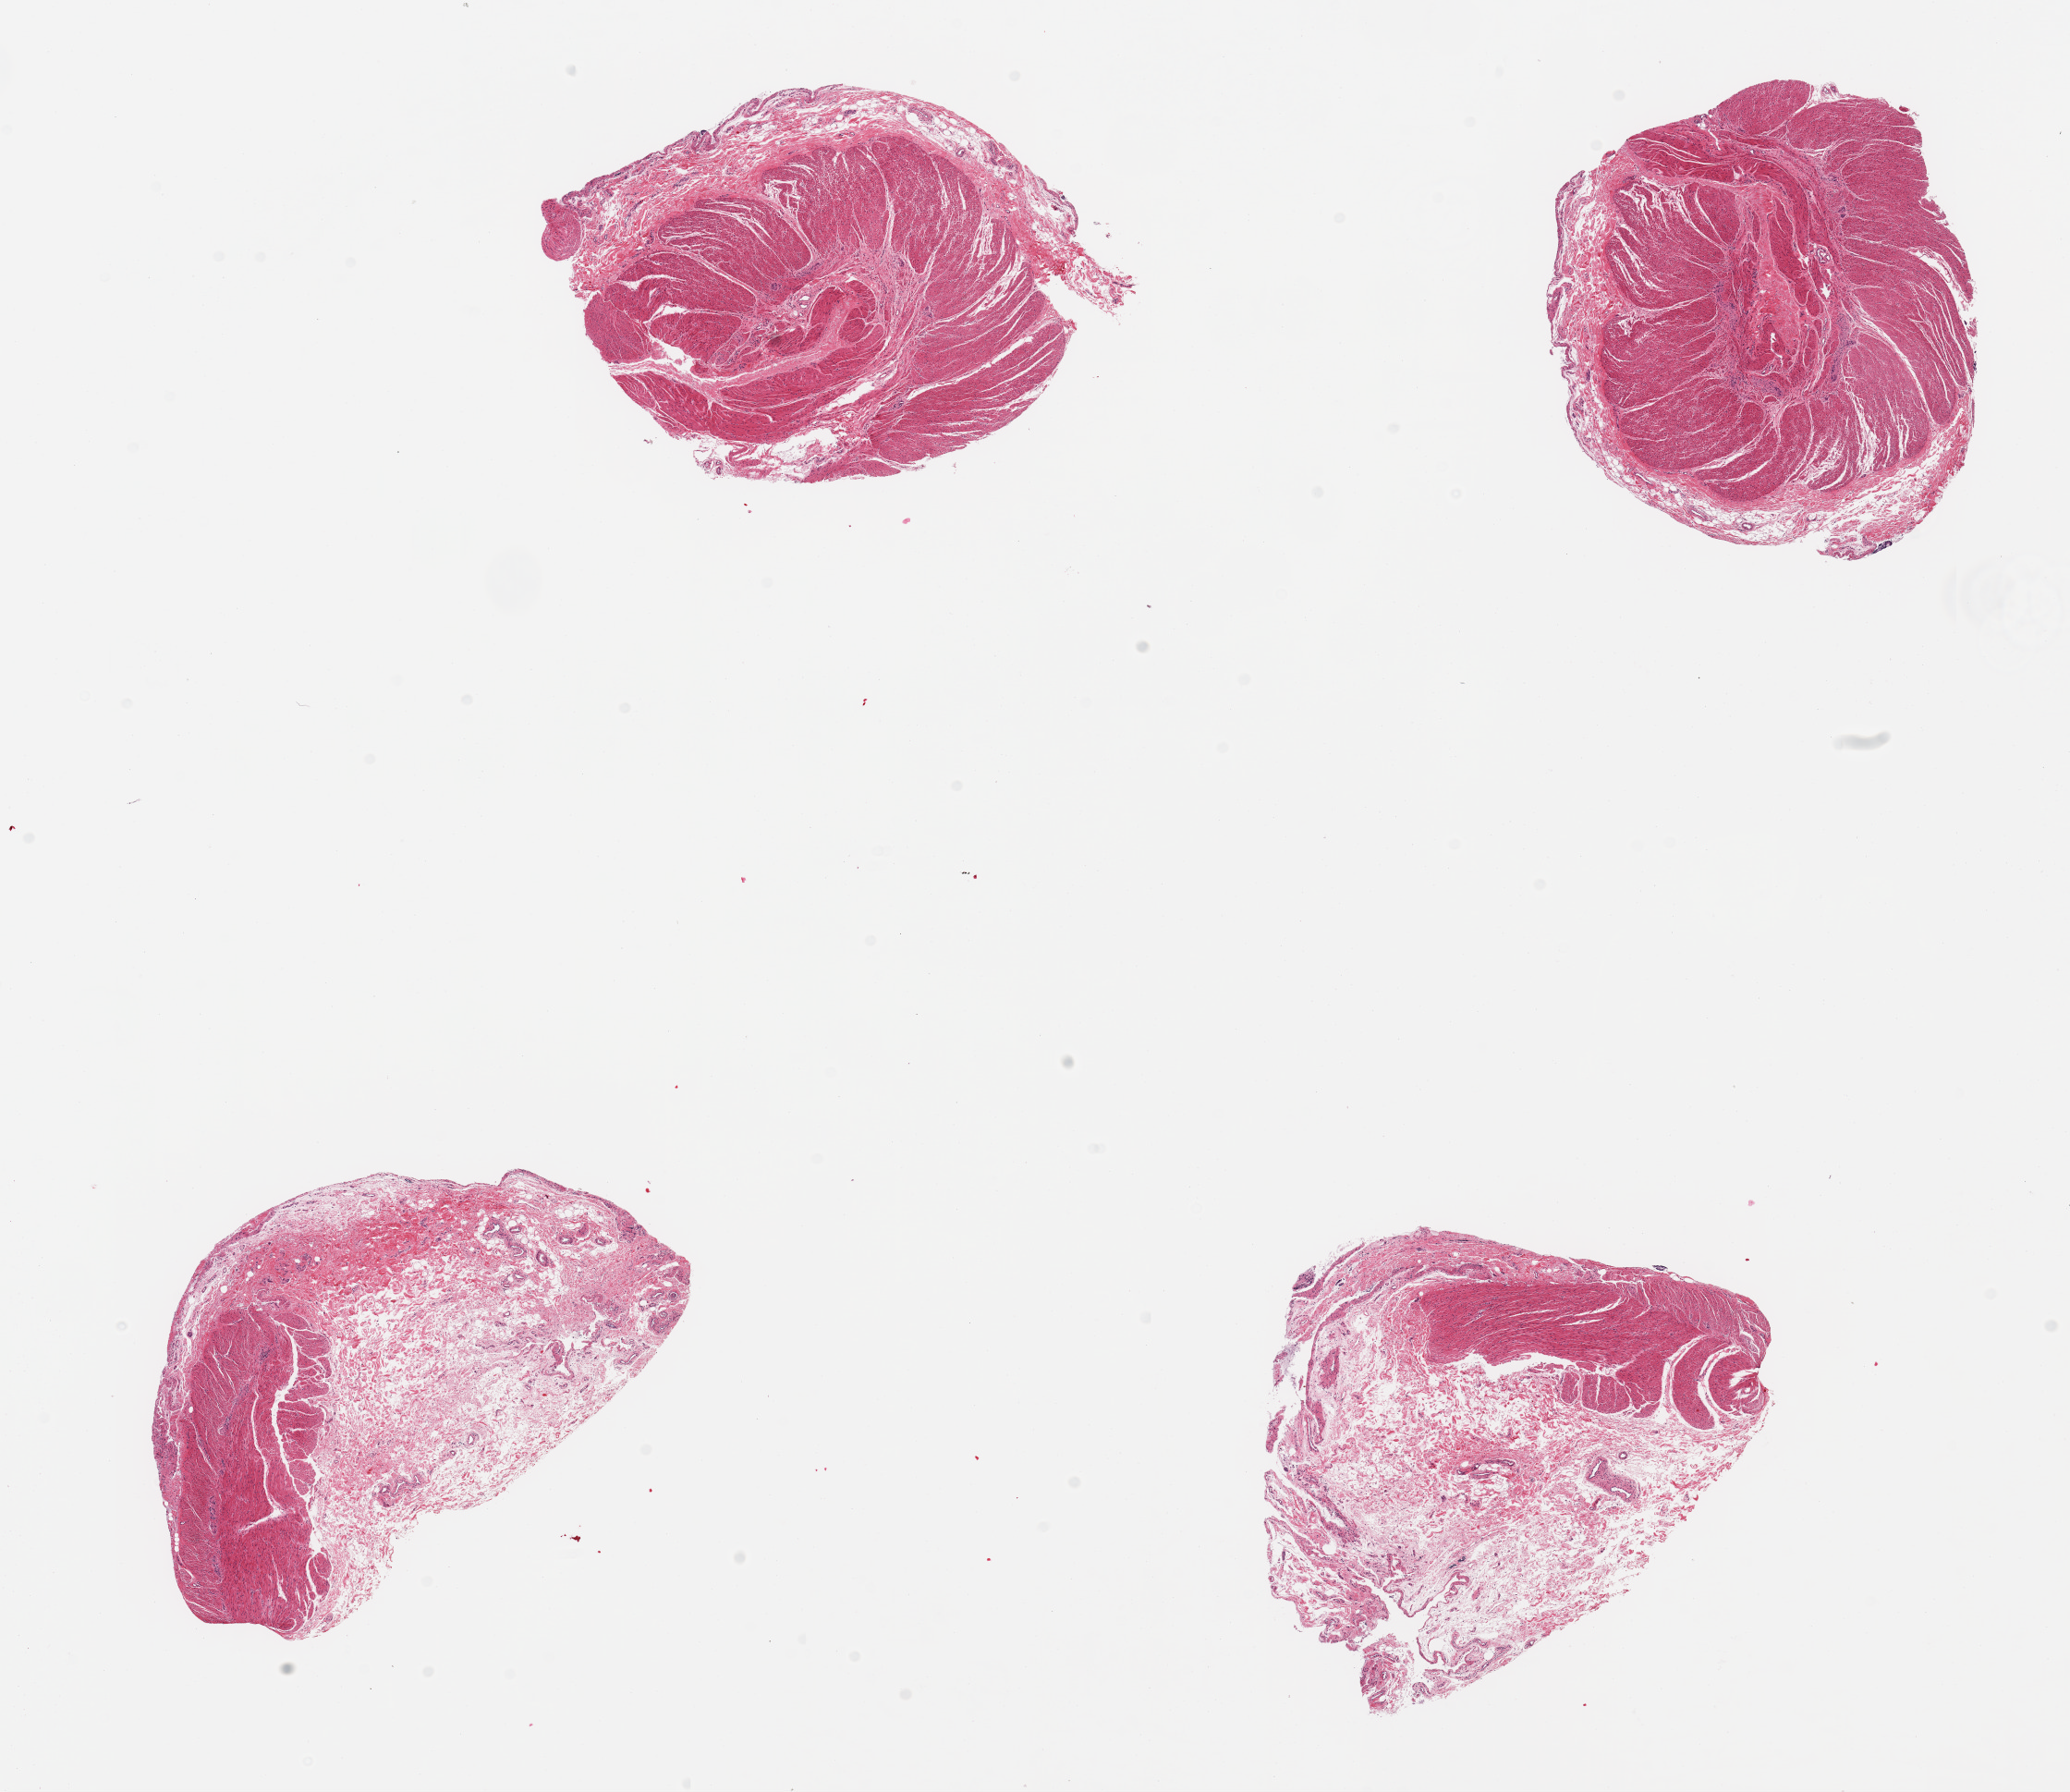
Whole-slide image, hematoxylin and eosin (H&E) stain, low-resolution overview of the scanned area, about 17.7 x 15.3 mm (acquisition: 20x scan). PAXgene-fixed paraffin-embedded (PFPE) section. Target tissue: sigmoid colon. Donor tissue sample. Male donor.
Review note (as recorded): 4 pieces; 2 have 80% & 60% submucosal fat.